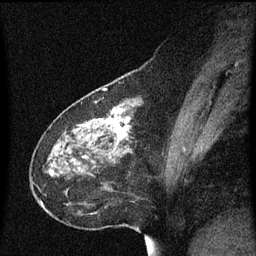
Breast MRI (dynamic contrast-enhanced), one sagittal slice; slice 23 of 60 in the series (ordered by position); dynamic contrast-enhanced series, image 2 of 3 at this slice position (ordered by acquisition); 1.5 T; TE 4.2 ms, TR 8.4 ms; 256 × 256 image matrix, field of view 200 × 200 mm. Patient: female, 49 years. Case-level facts recorded for this patient, not image findings: setting: breast cancer imaged before/during neoadjuvant chemotherapy; receptor status: HR-positive, HER2-negative.
Structures marked on this image (semi-automatically segmented with operator editing):
- analysis volume of interest (the breast-tissue region the enhancement analysis was run in; not a lesion): bounding box (x1, y1, x2, y2) in pixels: (31, 96, 171, 219)
- tumour enhancement mask (voxels above the 70 % enhancement threshold inside the analysis volume of interest): (107, 110, 129, 139)